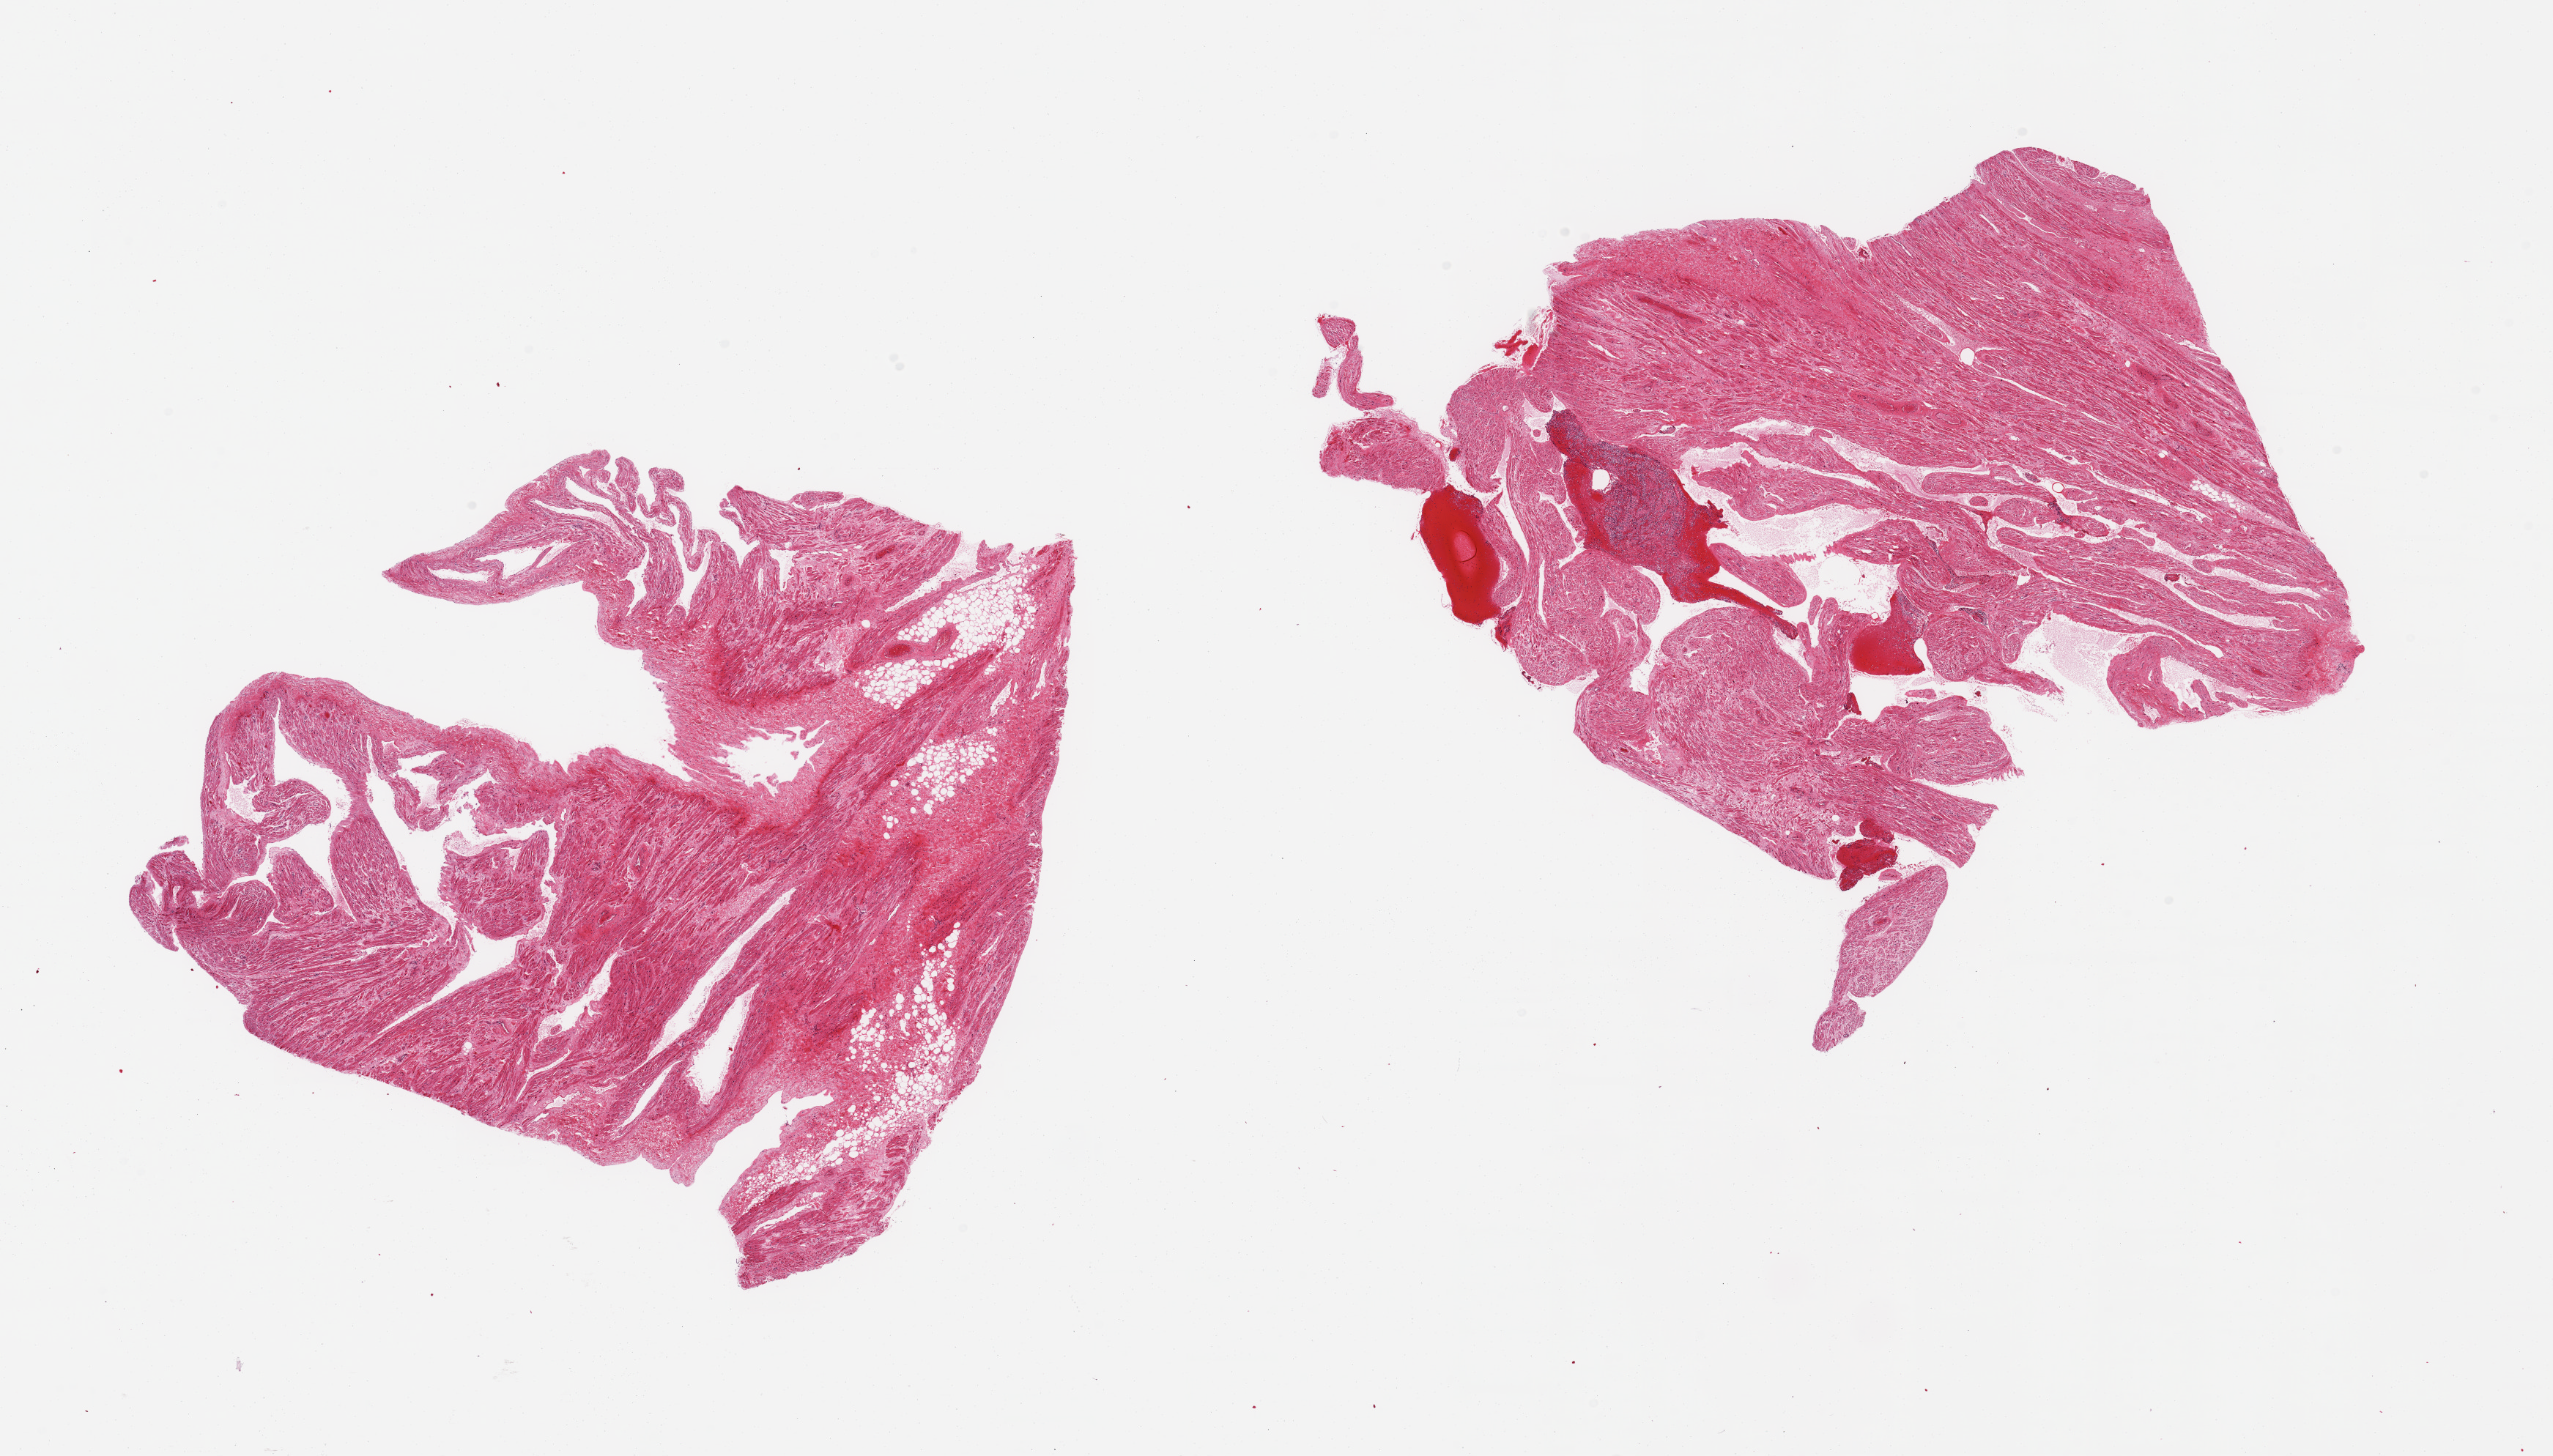
Hematoxylin and eosin (H&E) whole-slide image, brightfield — shown as a low-resolution overview of the whole scanned area (about 27.6 x 15.7 mm). PAXgene-fixed paraffin-embedded (PFPE) section. Sampled site (target tissue): auricular appendage. Tissue donor sample. Male donor.
- pathologist's review note for this sample: 2 pieces, no abnormalities